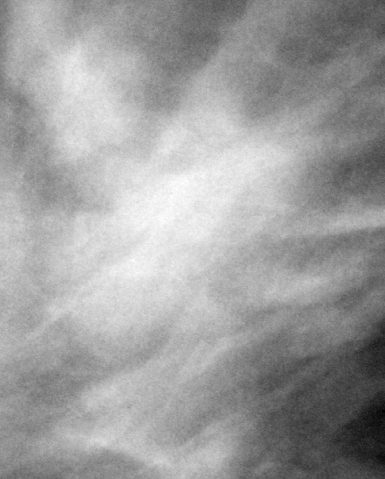
Region of interest cut from a scanned film mammogram (one marked finding), right breast, MLO view.
Mass, shape focal asymmetric density; BI-RADS assessment category 3; subtlety rating 5 on a 1 (subtle) to 5 (obvious) scale; benign without callback (not worked up further).